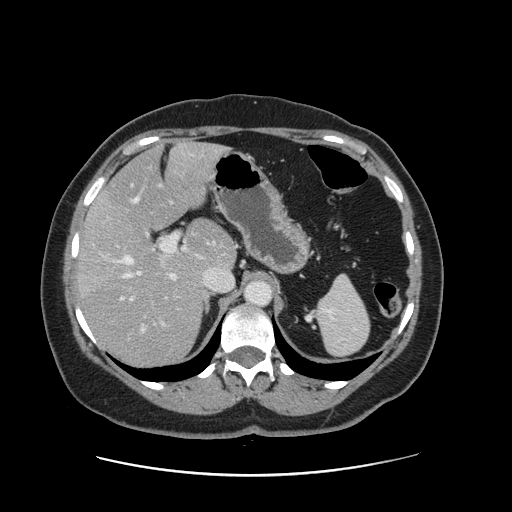
Contrast-enhanced abdominal CT, one axial slice. Position 97 of 161 along the scan axis. 120 kVp. Intravenous contrast given. Soft-tissue window (W 400 / L 40 HU). 2.5 mm slice thickness. 512 × 512 image matrix, field of view 398 × 398 mm. Female patient, age 62 years. From the clinical record (not read from this slice): diagnosis: colorectal cancer liver metastases, imaged before liver resection; multiple liver metastases: no; largest metastasis: 2.5 cm; disease in both lobes: no.
Annotated regions visible in this slice (expert manual segmentation):
- hepatic veins: bounding box <120,197,233,331> (left, top, right, bottom; pixels)
- liver: <80,143,235,365>
- planned liver remnant (the part of the liver to remain after resection): <104,143,235,269>
- portal vein (with intrahepatic branches): <128,234,195,339>